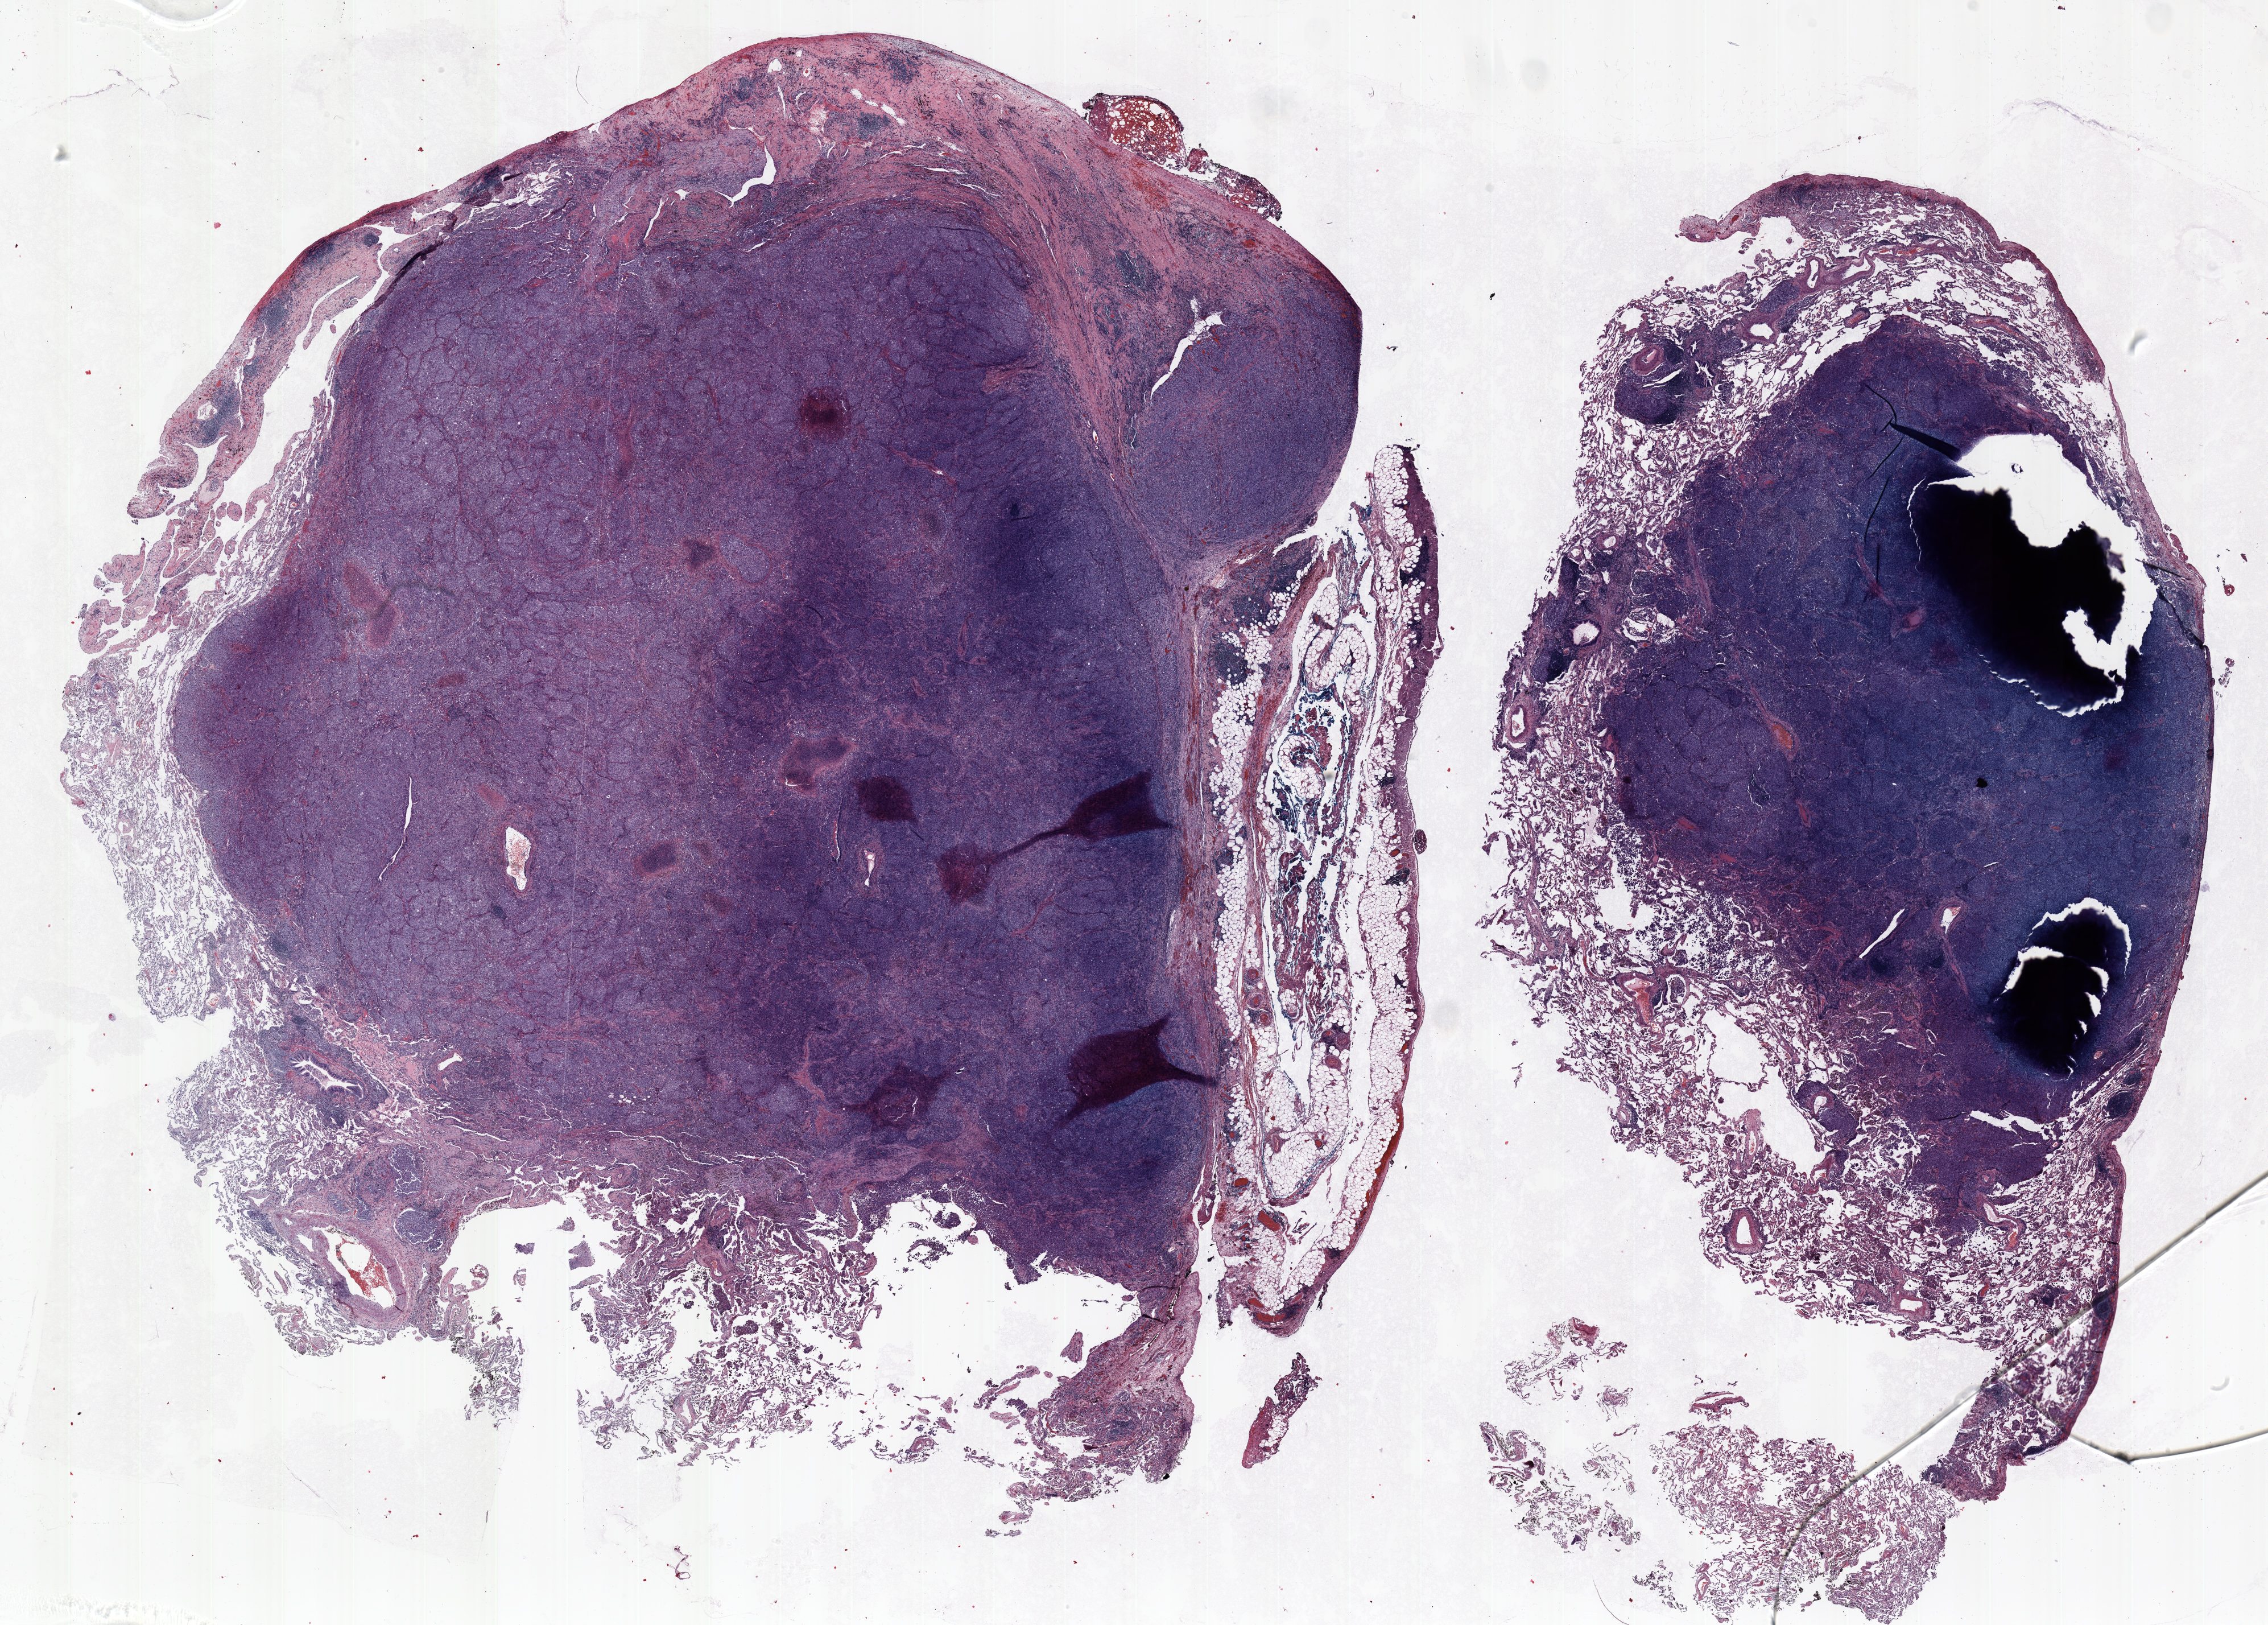
Whole-slide histology image, H&E-stained, a low-resolution overview of the entire scanned area, about 32.0 x 22.9 mm, FFPE section, lung. Male, age 63 at enrolment. Current smoker at enrolment. Grade: undifferentiated (G4).
- participant's lung-cancer diagnosis: Large cell carcinoma, NOS
- tumour size (pathology): 30 mm
- stage (AJCC 6th edition): IIIB
- primary tumour location (clinical record): left upper lobe